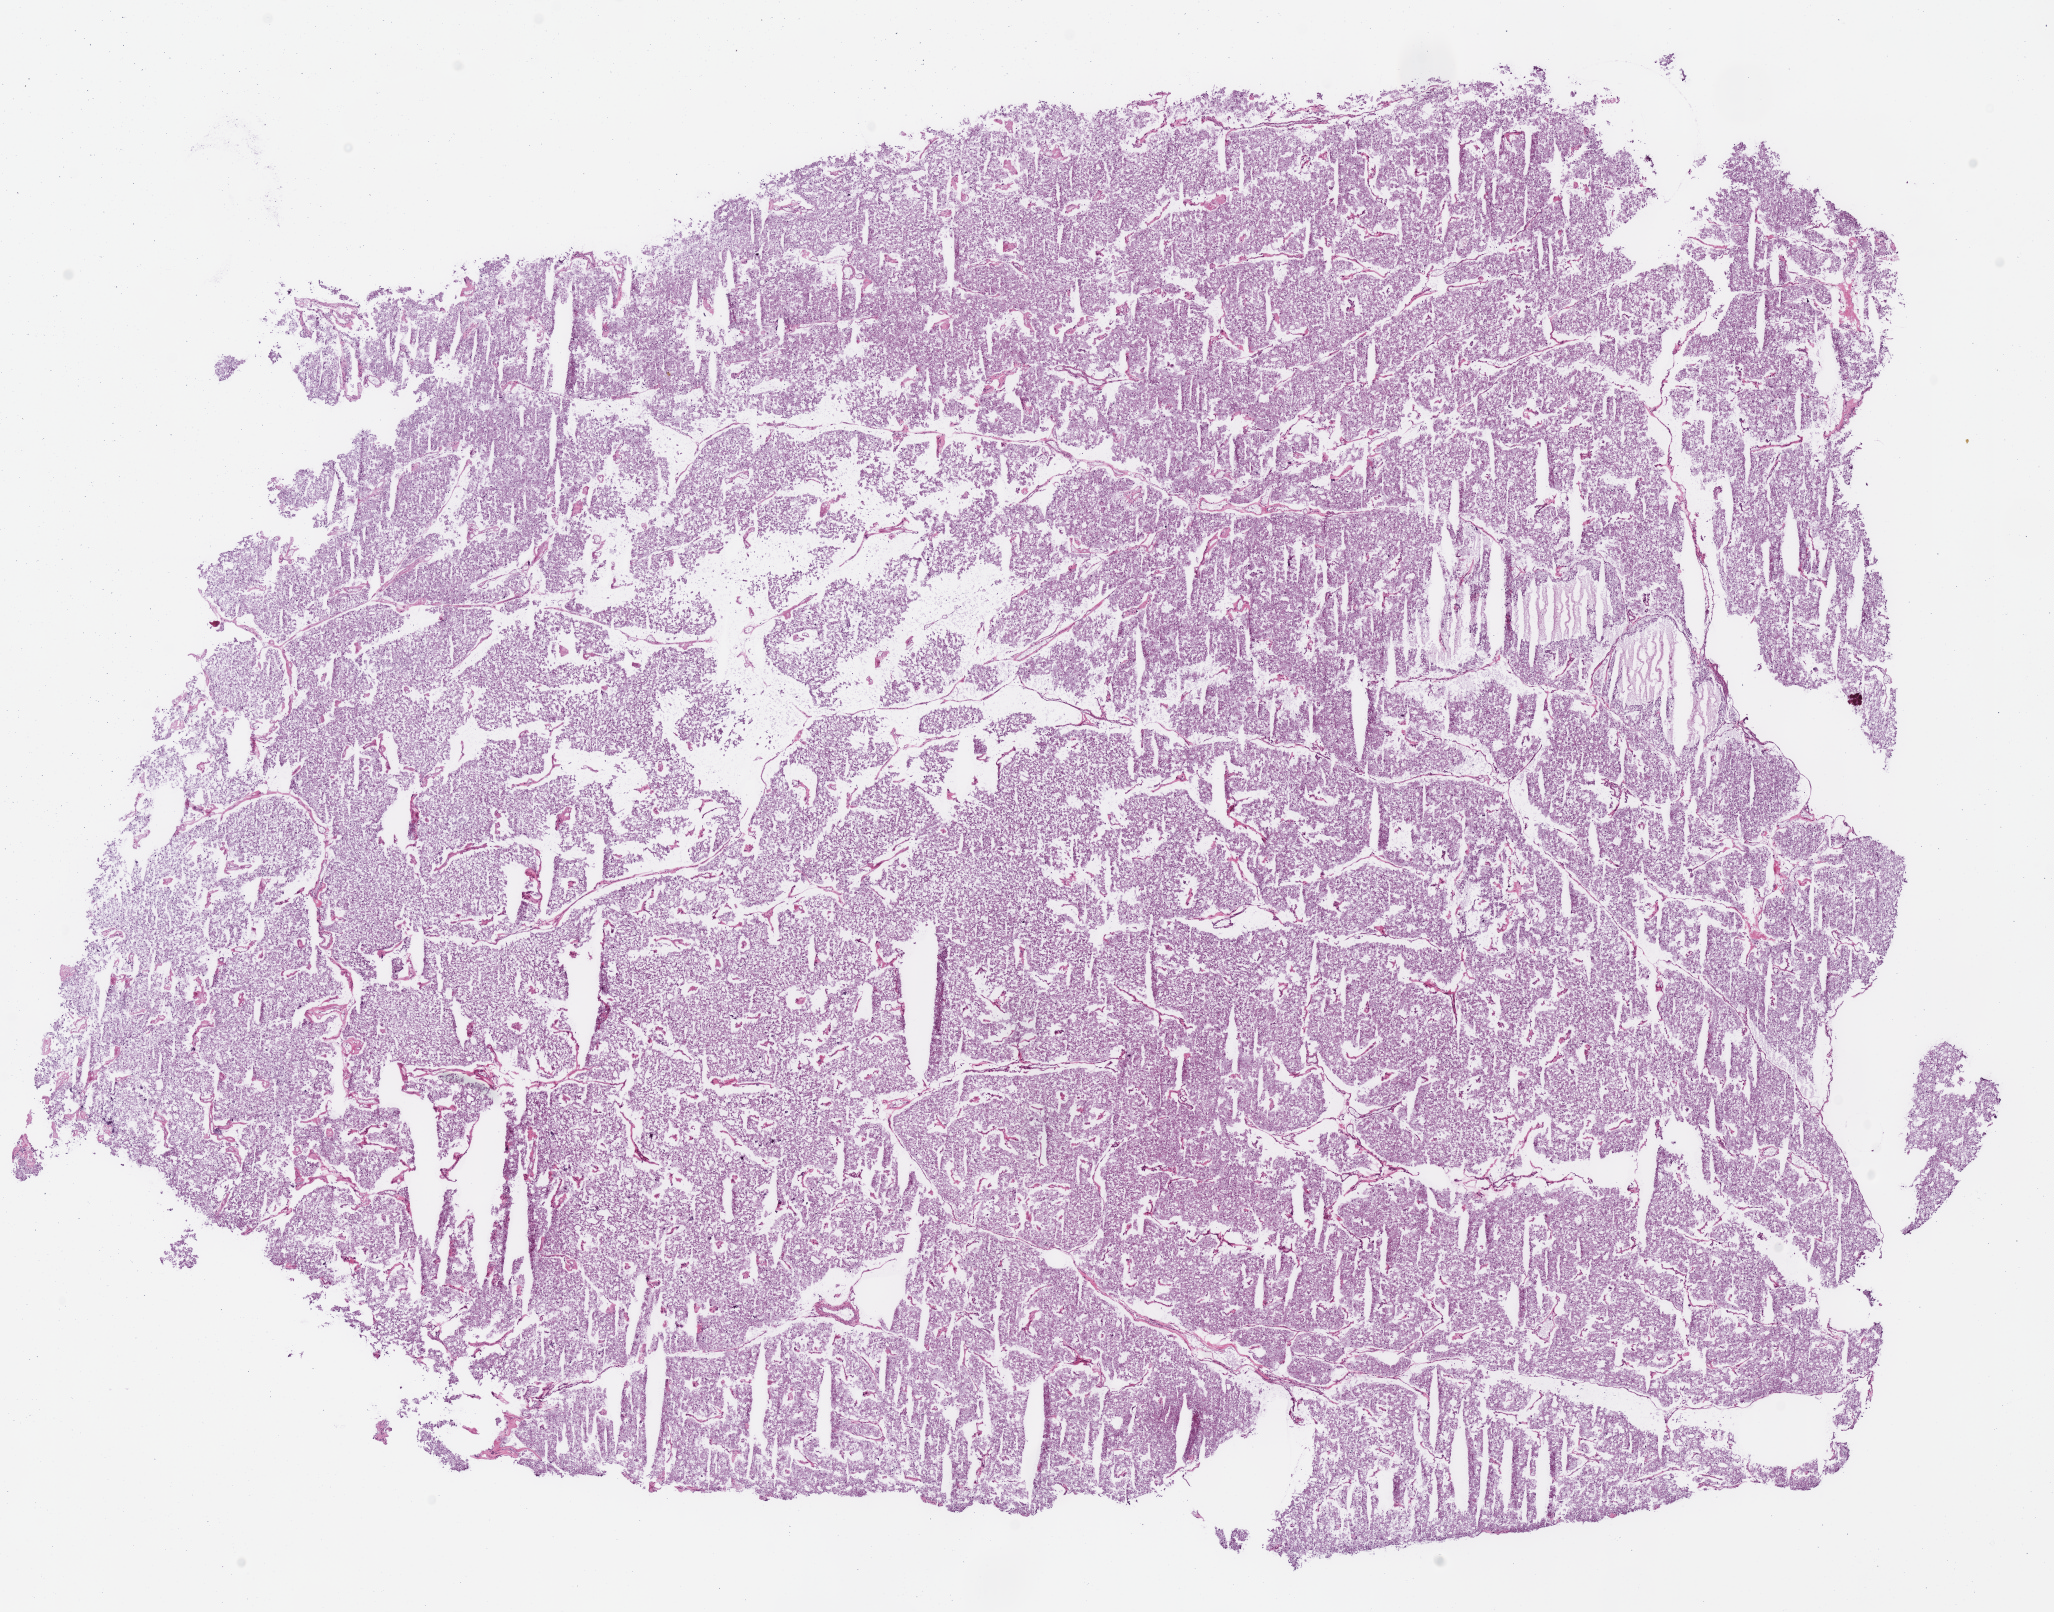
Whole-slide histology image, Hematoxylin and eosin (H&E) stained — shown as a low-resolution overview of the whole scanned area (about 16.2 x 12.7 mm); frozen section from the bottom of the tissue portion; sample: primary tumour, kidney. Patient: male, age at initial diagnosis 34 years. Composition of this section per pathologist review: tumour cells 95%, tumour nuclei 95%, normal cells 0%, stromal cells 5%, necrosis 0%.
- TNM: T2 N0 M0
- AJCC pathologic stage: II
- laterality: right
- diagnosis: Renal cell carcinoma, chromophobe type